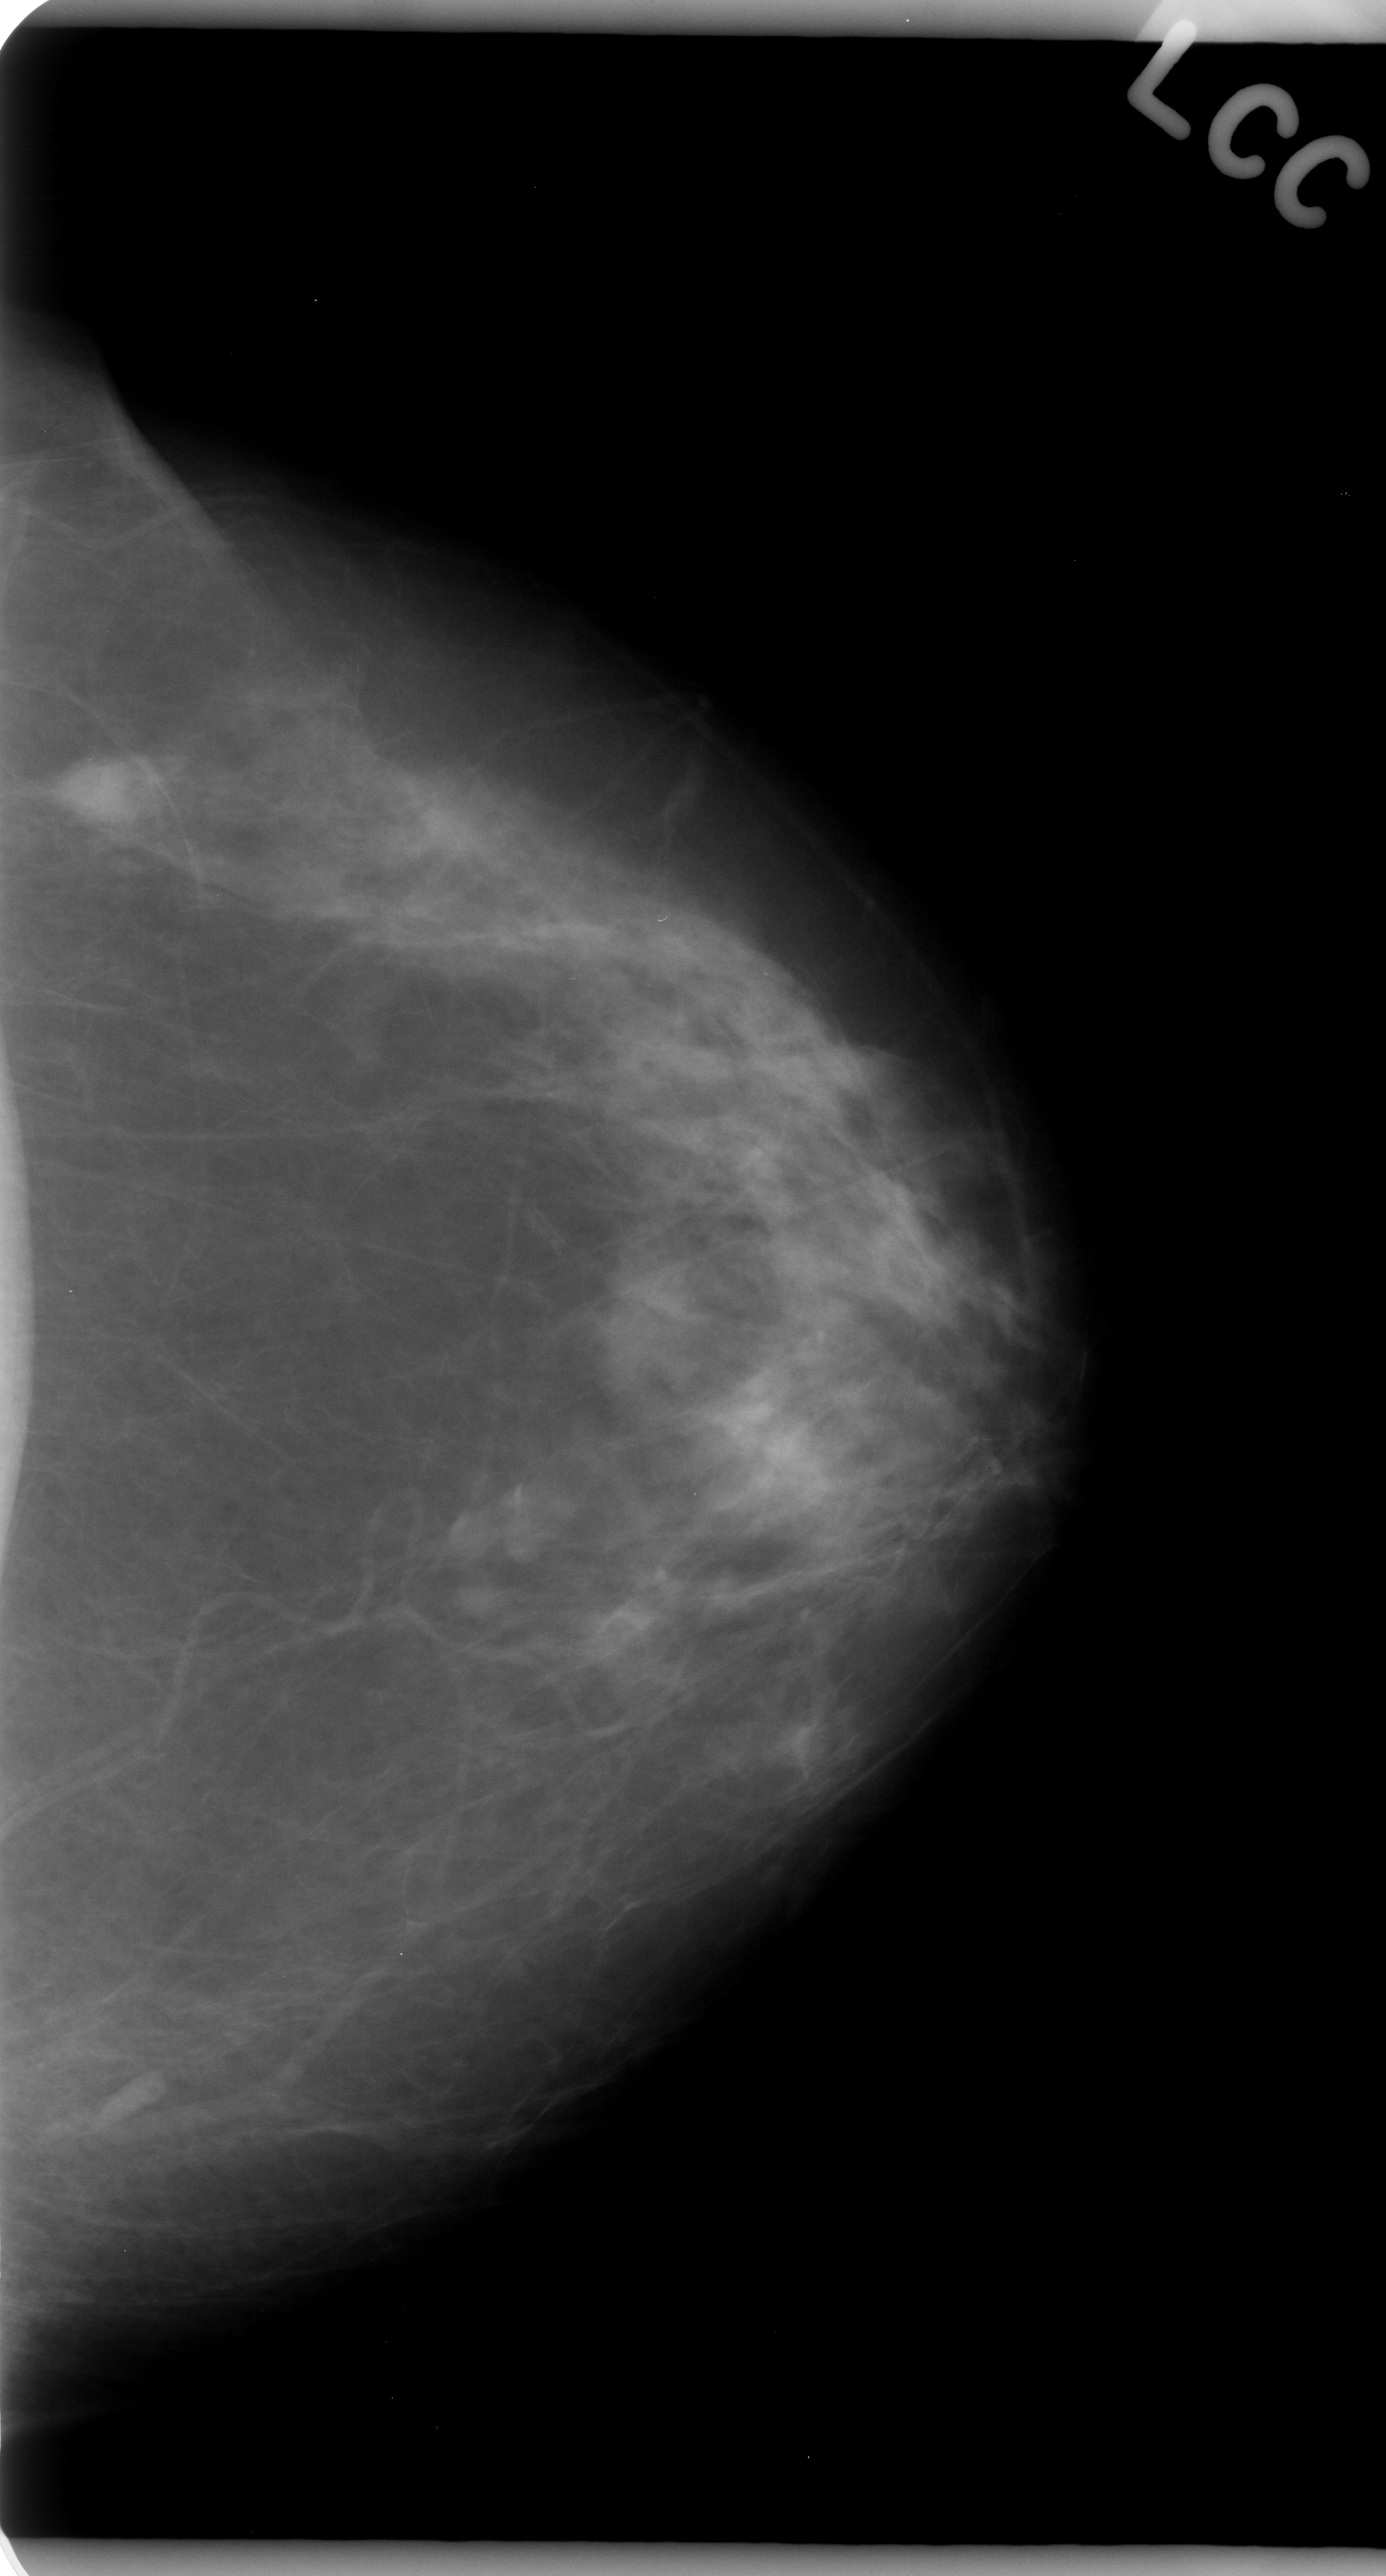
Scanned film-screen mammogram; left breast; craniocaudal (CC) view; 1386 × 2576 image matrix.
Marked abnormalities (boxes around the expert regions of interest):
- mass, shape oval, margins microlobulated; BI-RADS assessment category 4; subtlety rating 5 on a 1 (subtle) to 5 (obvious) scale; pathology (as recorded): malignant: bounding box <36,737,184,860> (left, top, right, bottom; pixels)